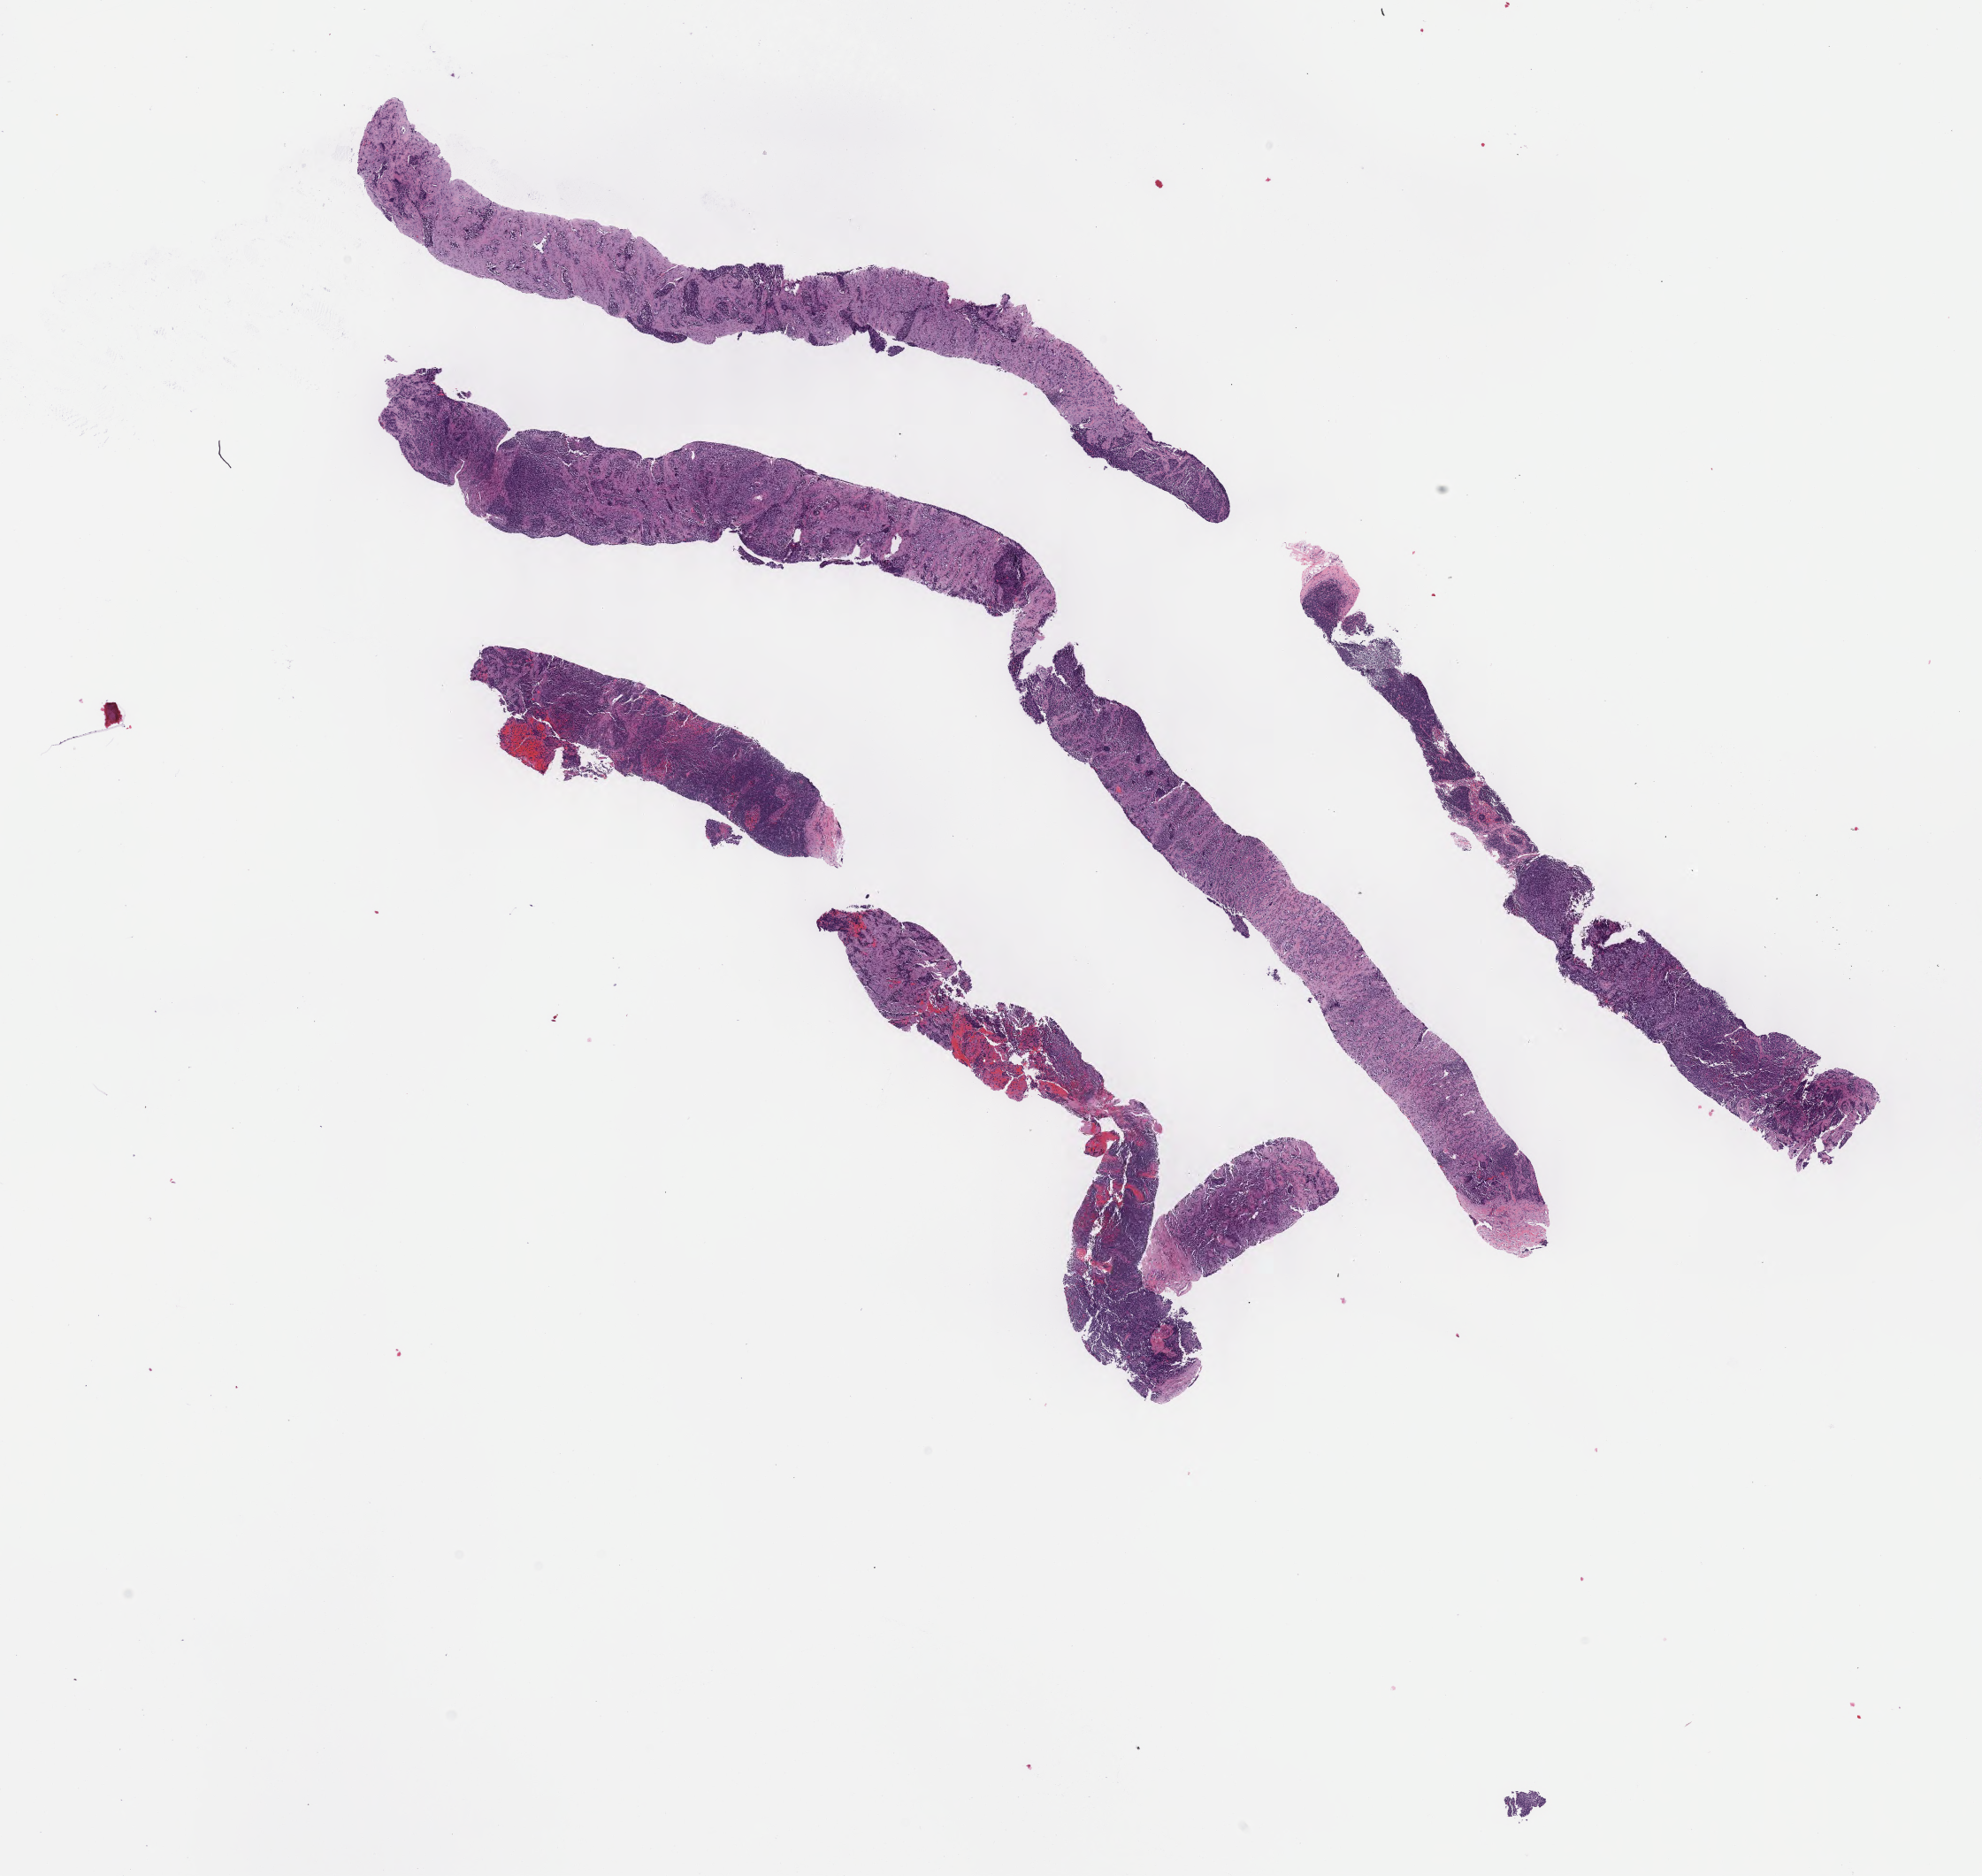
H&E whole-slide image of tumor tissue from the head and neck lymph node — a low-resolution overview of the entire scanned area, about 18.1 x 17.1 mm. Formalin-fixed, paraffin-embedded (FFPE) tissue. Male patient, age 224 months (18 years 8 months).
Recorded diagnosis: Rhabdomyosarcoma, NOS.